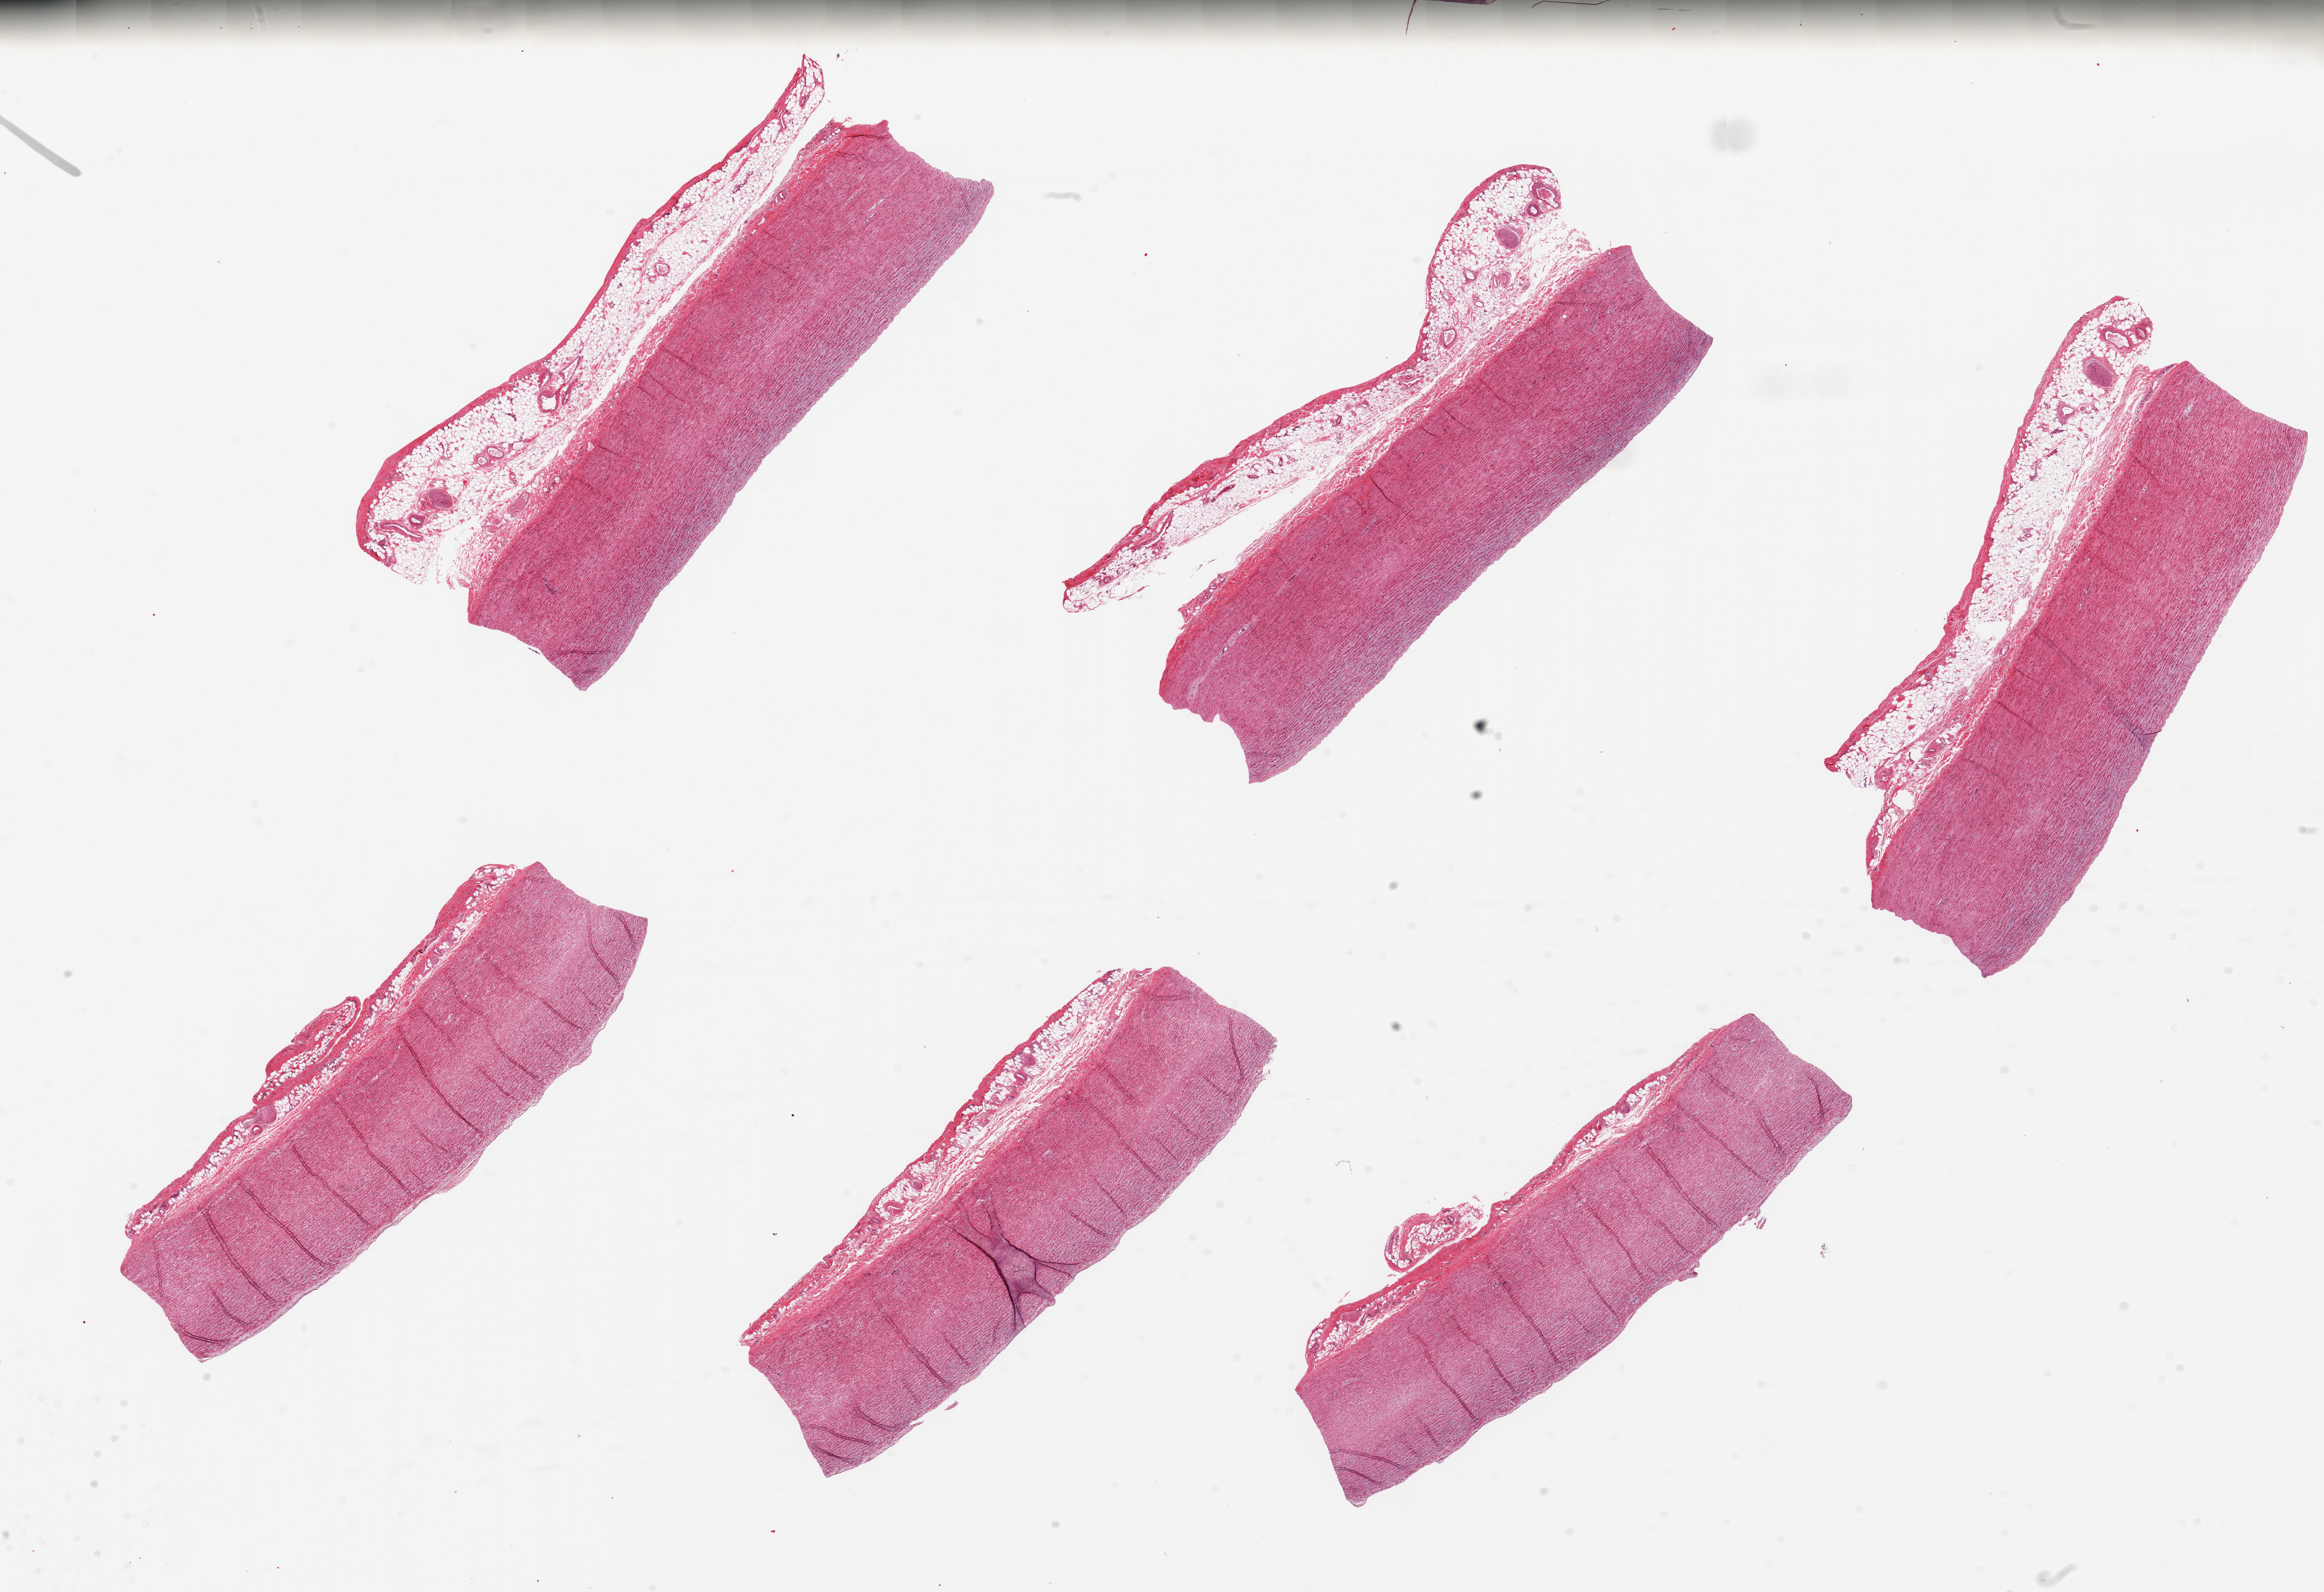
Digitized haematoxylin and eosin-stained section, low-resolution overview of the scanned area, about 30.5 x 20.9 mm; PAXgene-fixed paraffin-embedded (PFPE) section; target tissue: aorta; donor tissue sample. Donor: male.
Reviewer comment on this tissue sample: 6 pieces, up to 9x4mm; 2mm wall and about 1 mm extraneous adipose; no plaques.